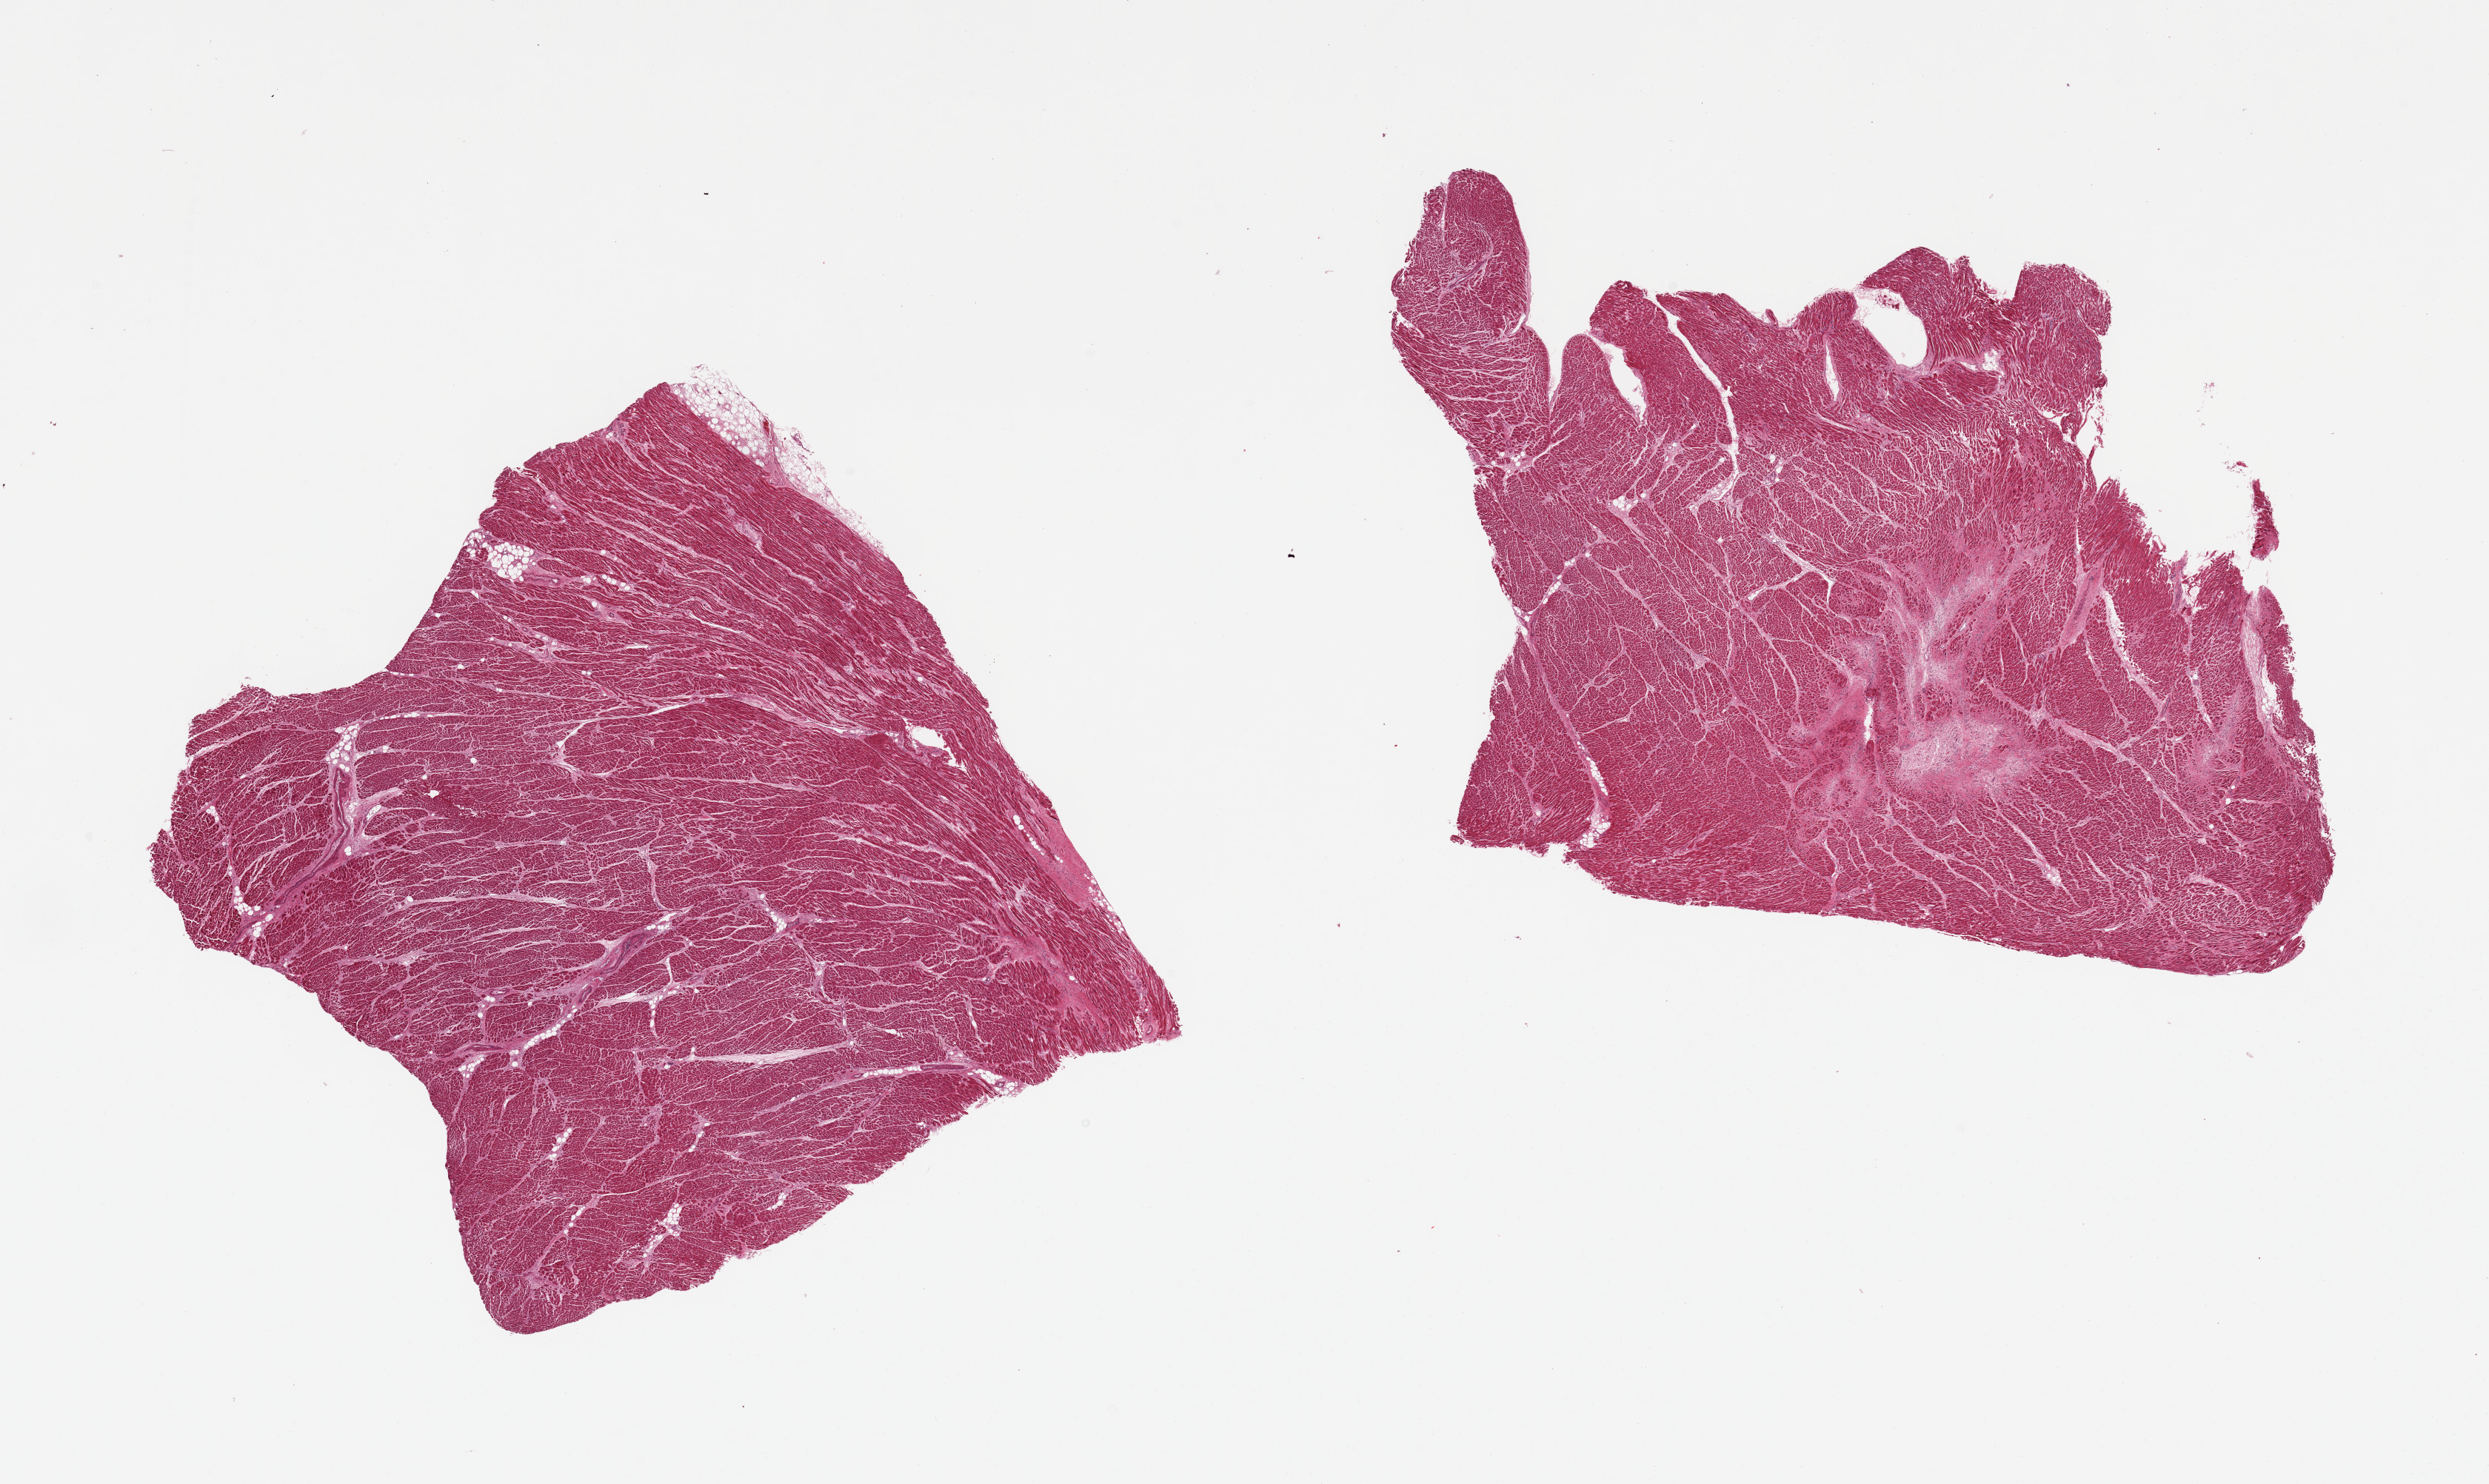
Whole-slide image, hematoxylin and eosin (H&E) stain — whole scanned area (about 26.6 x 15.8 mm) shown as a low-resolution overview. PAXgene-fixed paraffin-embedded (PFPE) section. Sampled site (target tissue): heart. Tissue donor sample.
Pathologist's review note for this sample: 2 pieces patch of fibrosis c/w prior infarction, increased interstital fibrosis.